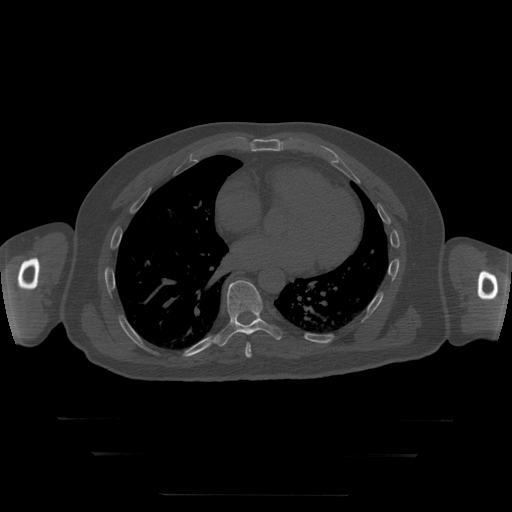
CT including the spine, one axial slice. Position 147 of 397 along the scan axis. Reconstruction kernel STANDARD. 120 kVp. Bone window (W 1800 / L 400 HU). 512 × 512 image matrix, field of view 510 × 510 mm. Patient age 73 years. Case-level facts recorded for this patient, not image findings: primary cancer: prostate.
Structures marked on this image (semi-automatically segmented with operator editing):
- T8 vertebra: bounding box [x1, y1, x2, y2] px = [245, 343, 252, 358]
- T9 vertebra: [214, 281, 282, 347]